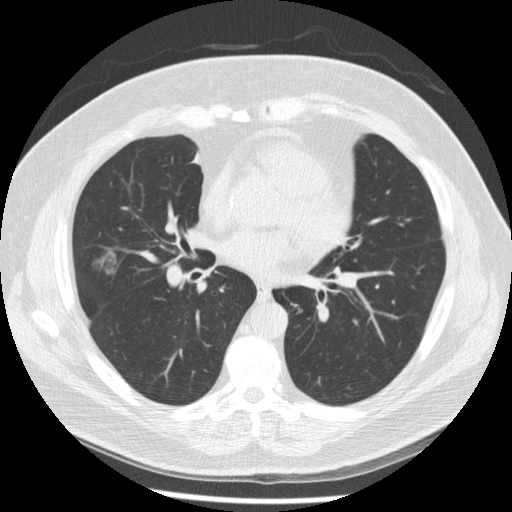
Chest CT (low-dose screening protocol), one axial image, second annual screen, lung window (W 1500 / L -600 HU), standard (soft-tissue) reconstruction kernel (STANDARD), slice 120 of 230 in the series. Male, age 67 years at enrolment. Former smoker at enrolment.
Expert-annotated lung lesion, bounding box <78,244,125,287> (left, top, right, bottom; pixels). Reader record for this screening exam (exam-level; its link to the box is not recorded): non-calcified nodule or mass ≥4 mm, right middle lobe, 19 × 16 mm, smooth margins, soft tissue attenuation, pre-existing on the prior screen: yes; interval growth: yes. Lung cancer was diagnosed 47 days after this screen: adenocarcinoma, NOS, right middle lobe, moderately differentiated (G2), stage IA (AJCC 6th edition), 14 mm at pathology.